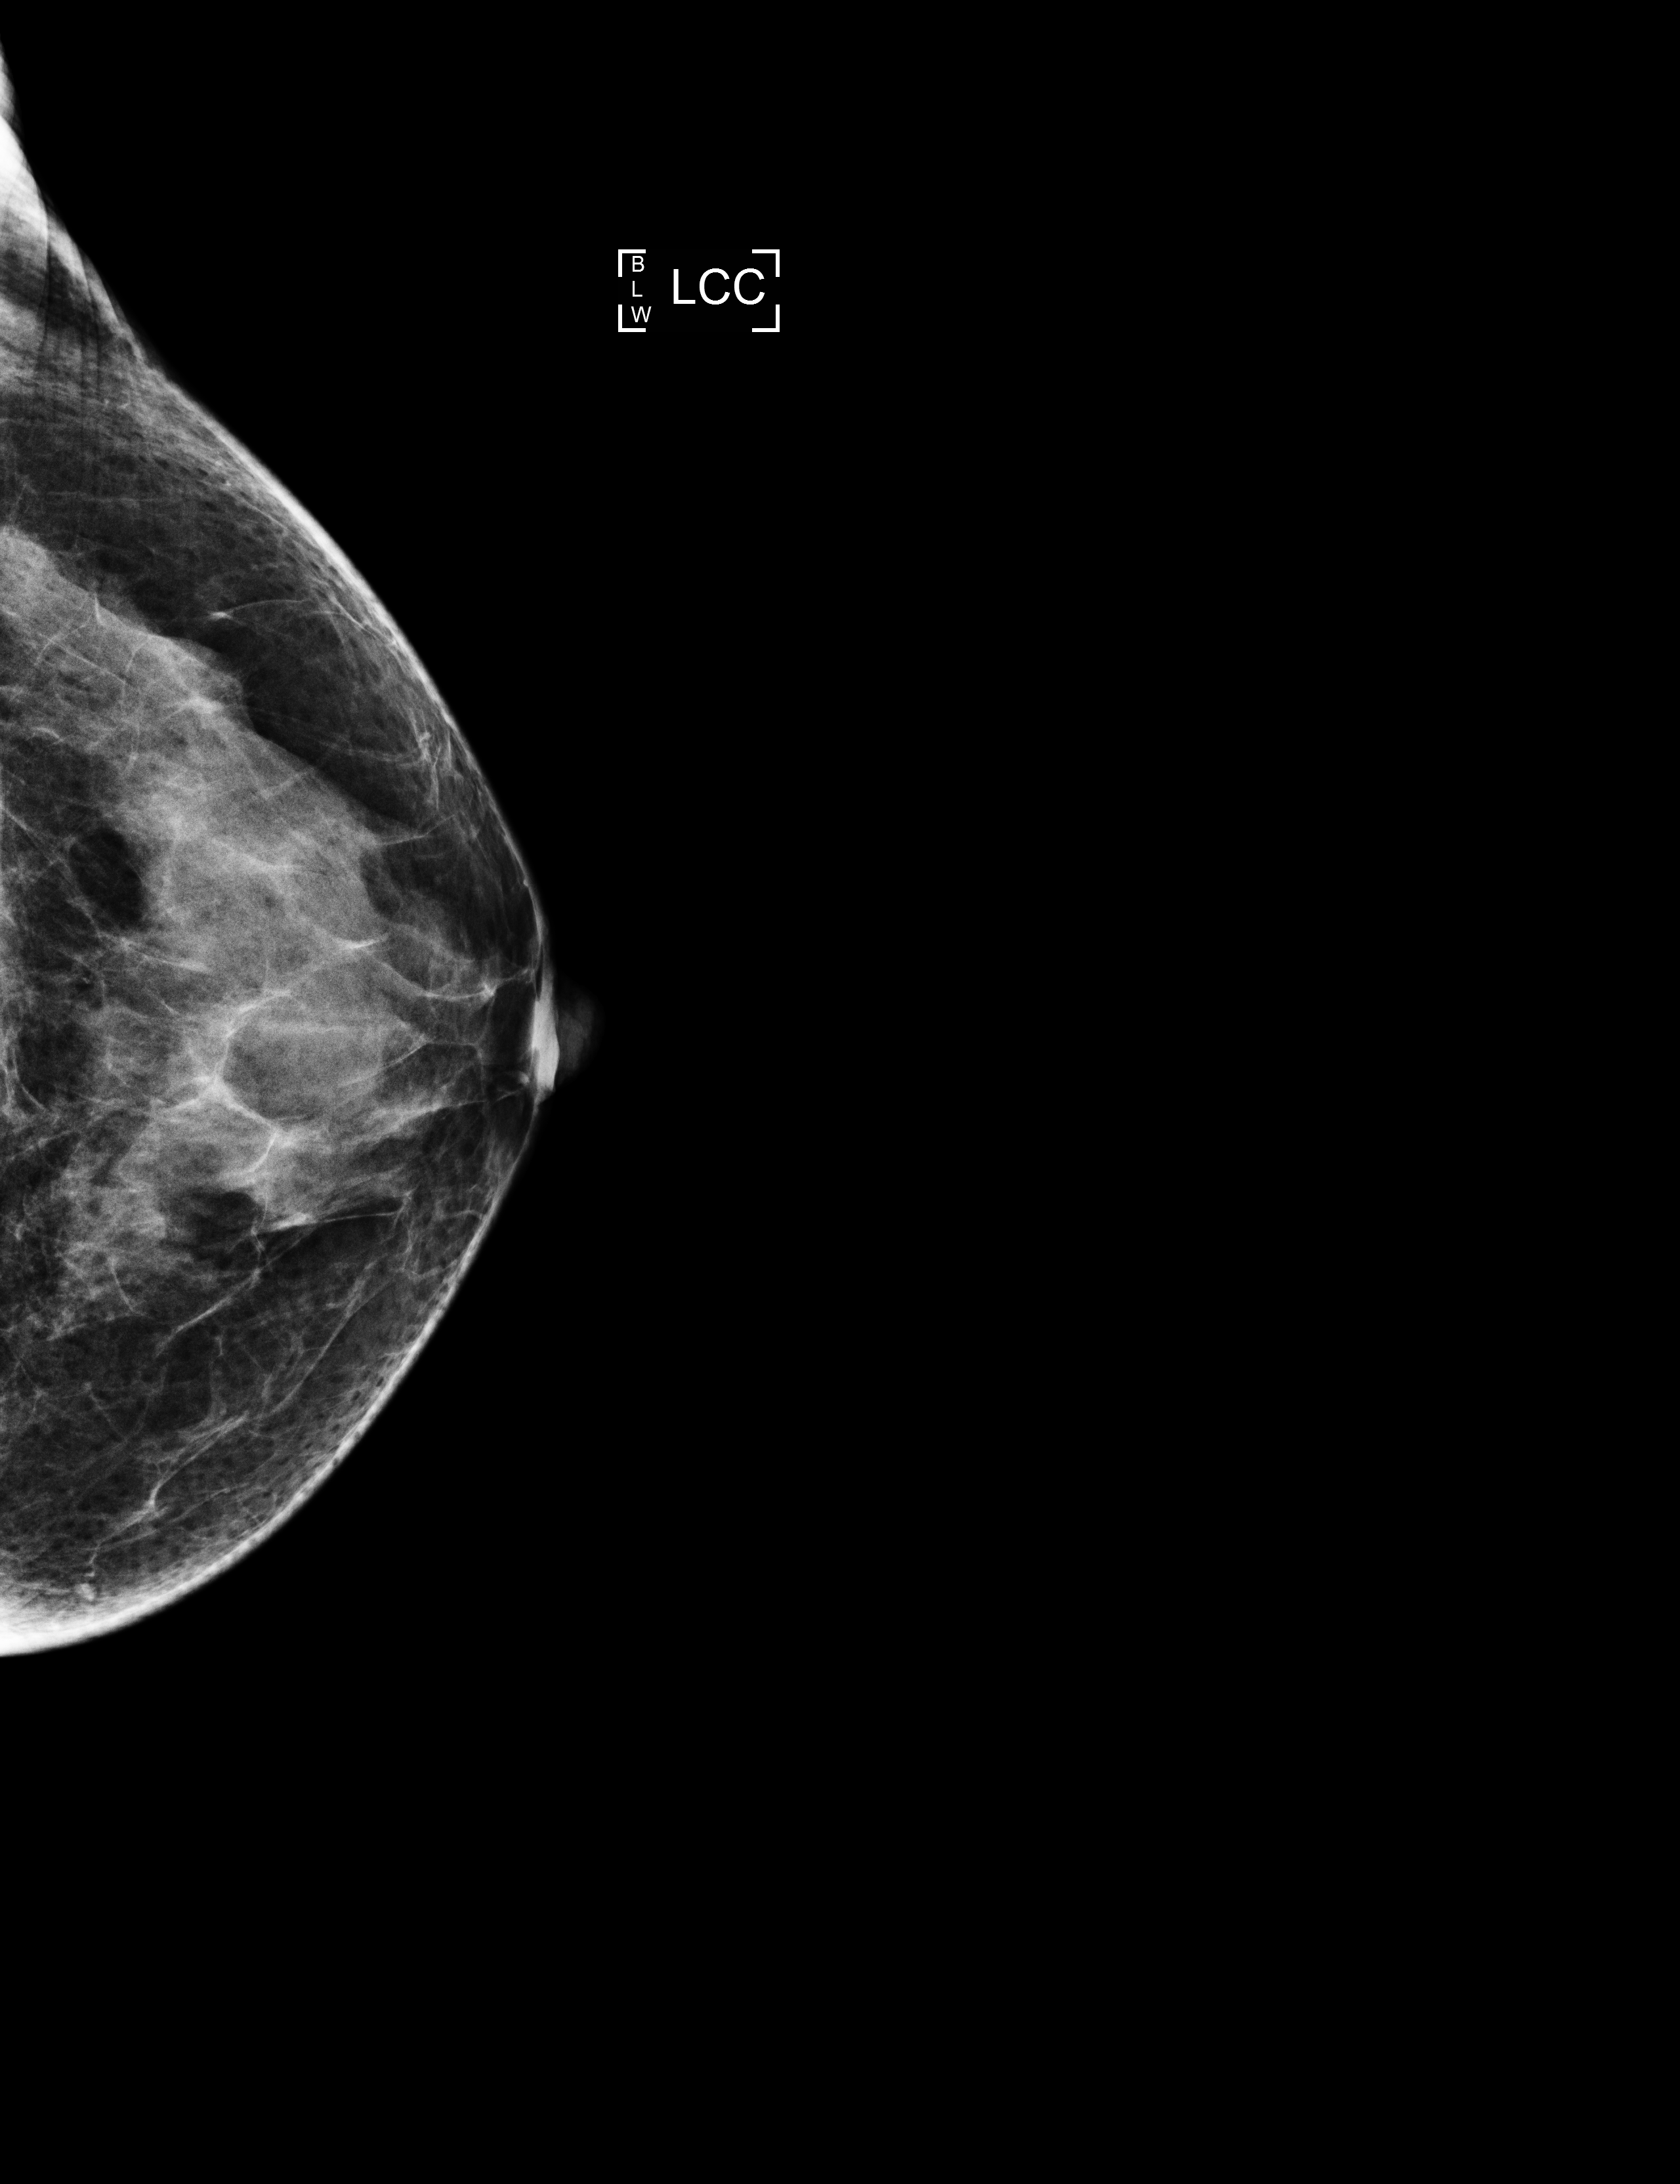
Screening examination, system: Selenia Dimensions. Patient: female, 58 years.
Image type: full-field digital mammogram. Breast: left. Projection: CC view.